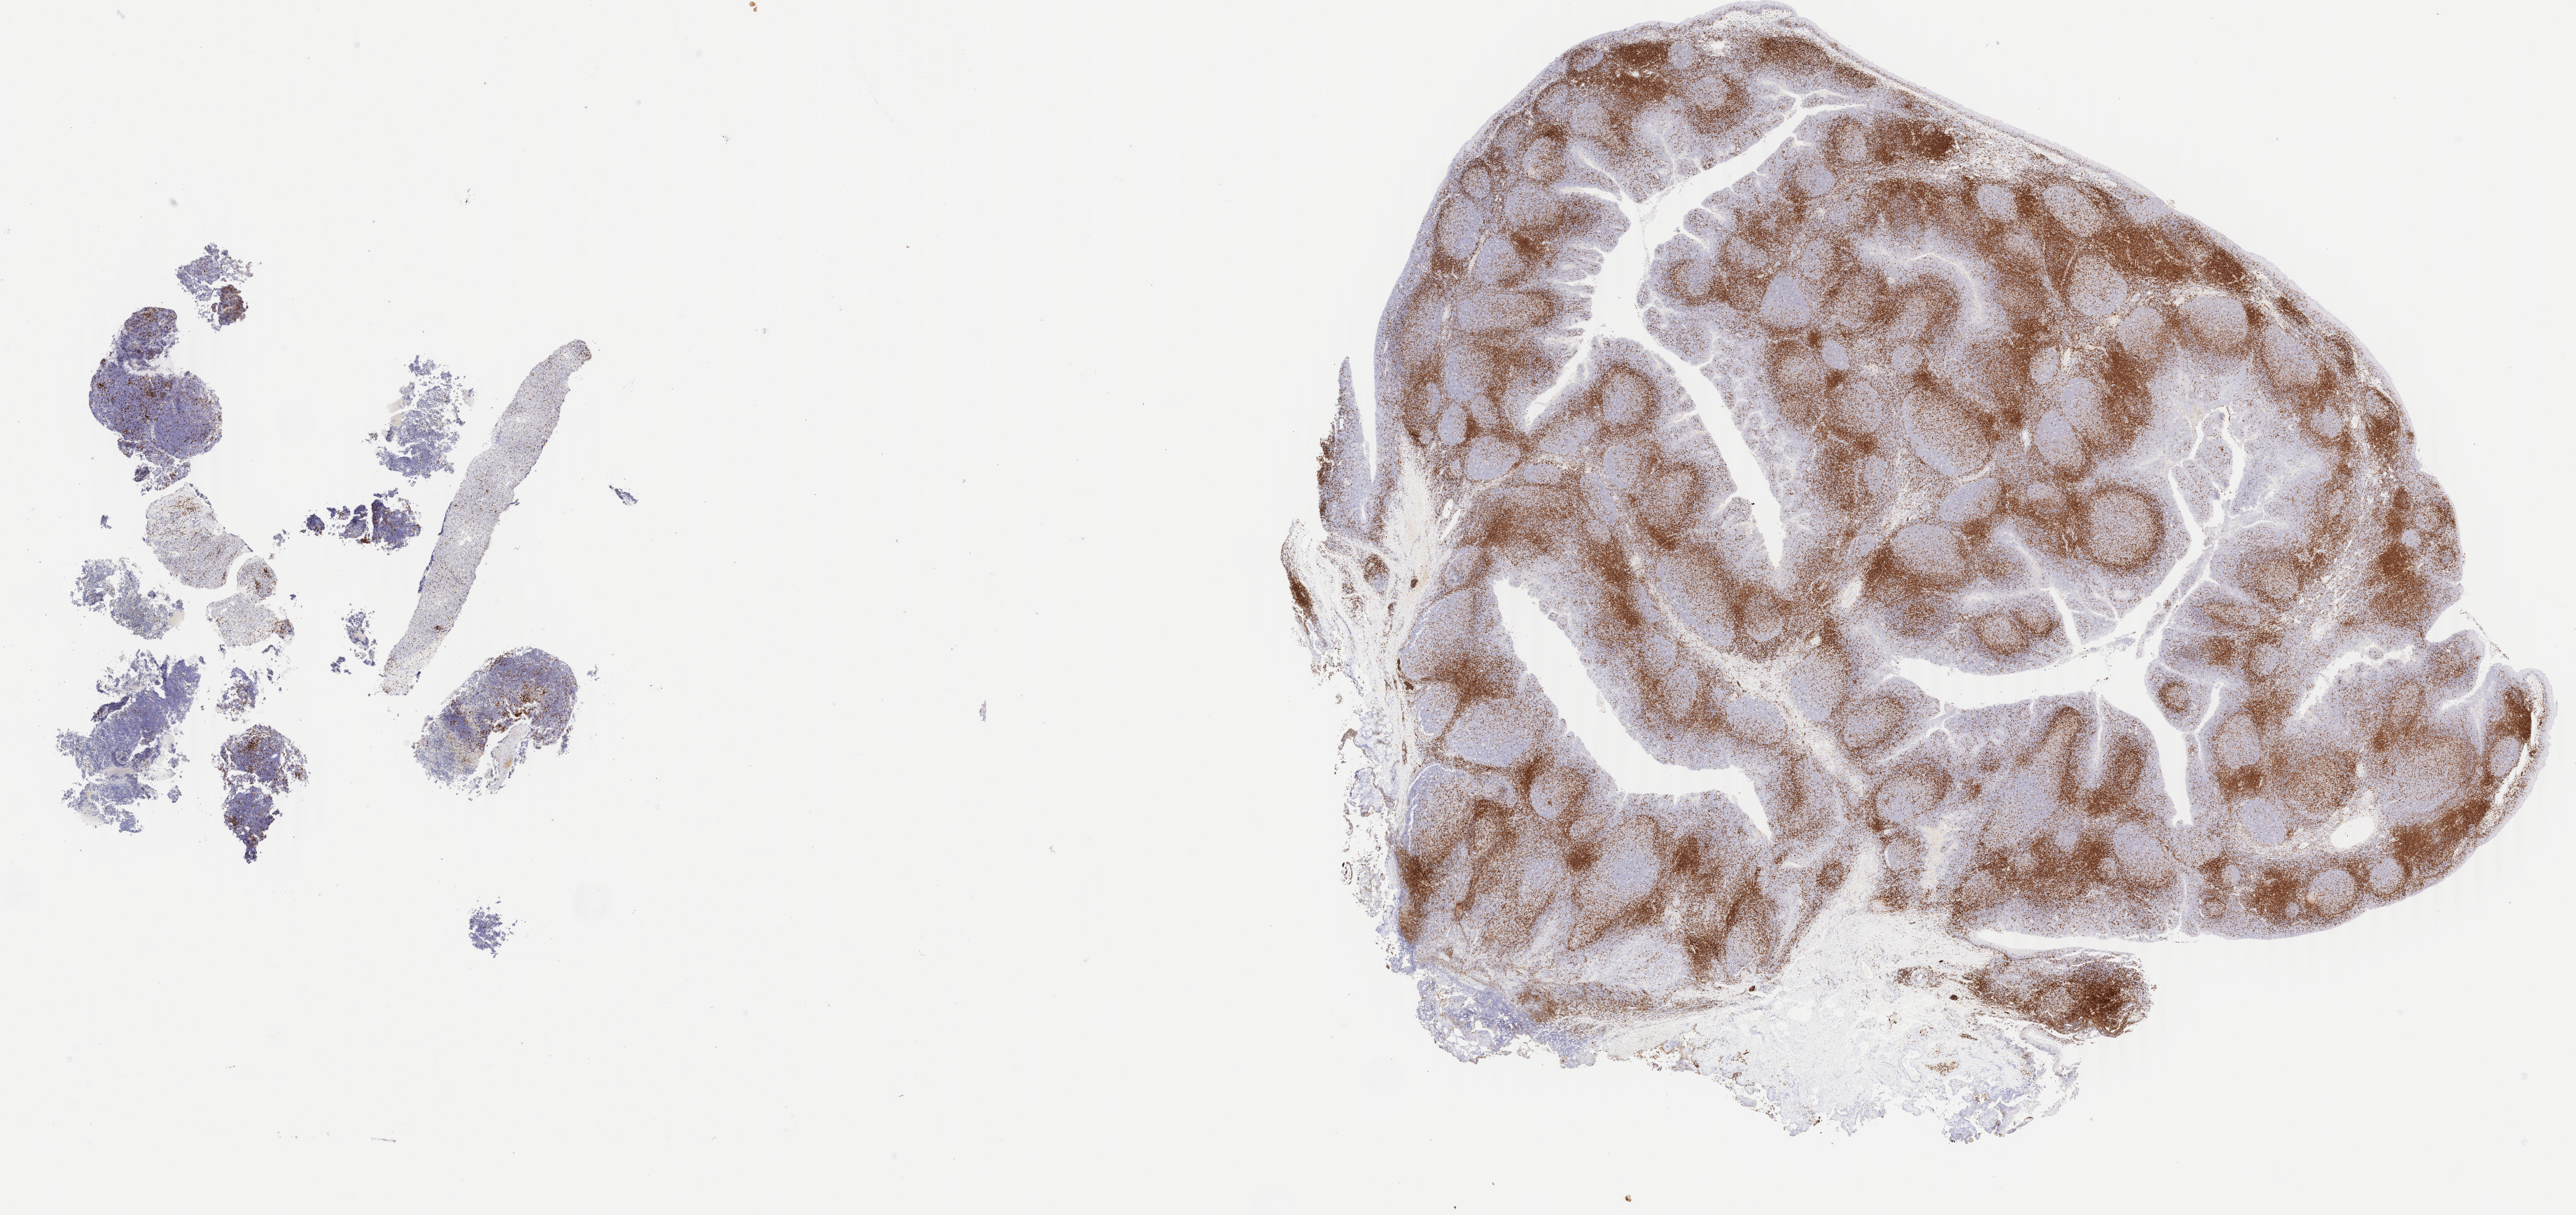
Whole-slide image, immunohistochemical stain for CD3 — shown as a low-resolution overview of the whole scanned area (about 29.3 x 13.8 mm); specimen: tumor tissue; anatomic site: liver. Male patient; age at initial diagnosis 5 years.
Histologic diagnosis: Burkitt lymphoma, NOS.